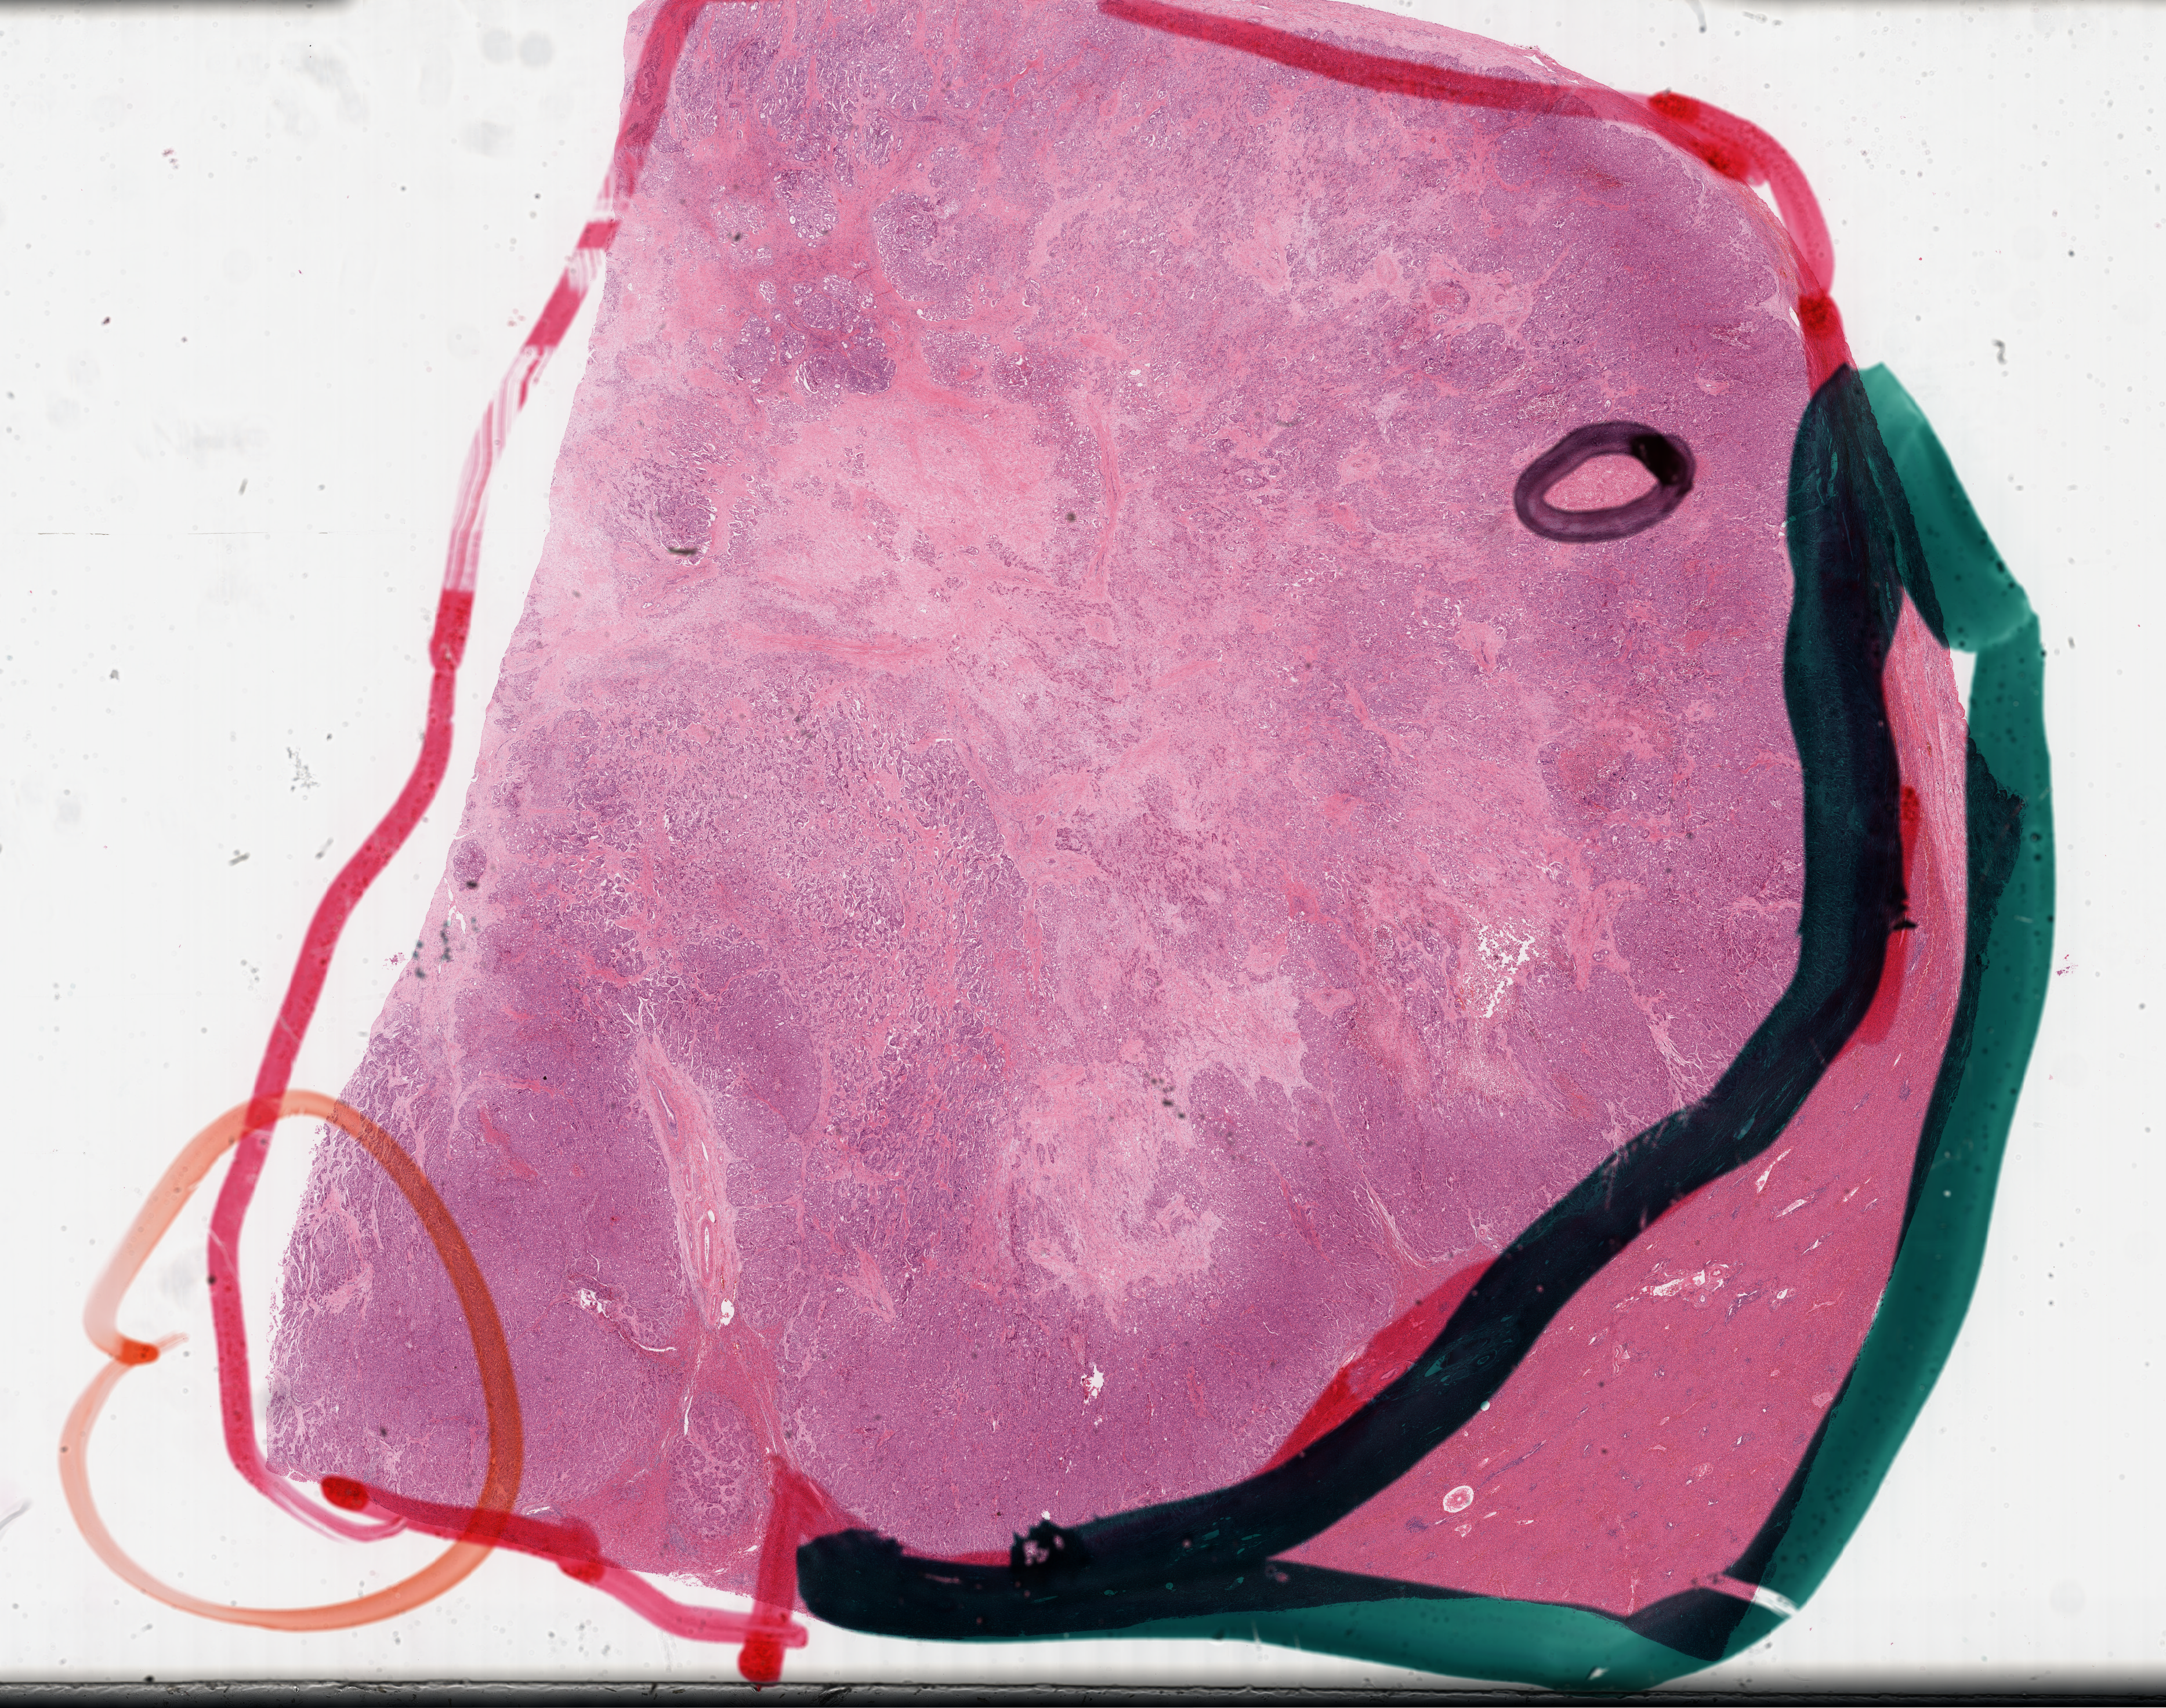
H&E whole-slide image, low-resolution overview of the scanned area, about 30.2 x 23.8 mm (from a 40x scan), formalin-fixed paraffin-embedded (FFPE) diagnostic section, liver, primary tumour sample. Female patient; age at initial diagnosis 60 years. Histologic grade: G2 (moderately differentiated).
- histologic diagnosis: Hepatocellular carcinoma, NOS
- AJCC pathologic stage: IIIA (7th edition)